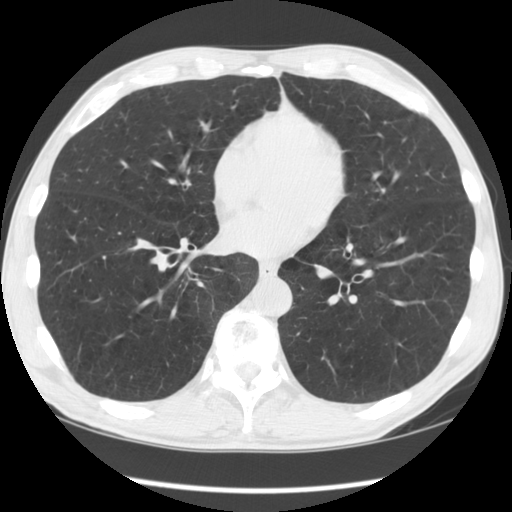
Low-dose screening chest CT, one axial slice; position 48 of 135 along the scan axis; lung window (W 1500 / L -600 HU); 2.5 mm slice thickness; 512 × 512 image matrix.
Outlined on this slice (expert manual segmentation):
- lesion 1 (tumor, lower lobe of right lung): bounding box [x1, y1, x2, y2] px = [137, 238, 153, 247]